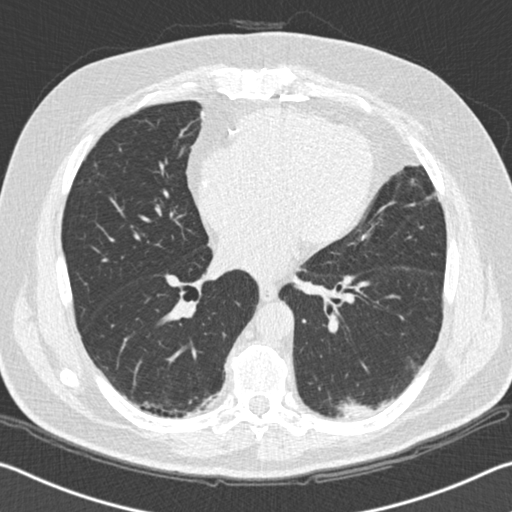
Chest CT (low-dose screening protocol), one axial image, second screening round (one year after baseline), lung window (W 1500 / L -600 HU), standard (soft-tissue) reconstruction kernel (B30f), 120 kVp, slice 91 of 172 in the series, 512 × 512 image matrix. Male, age 65 years at enrolment. Former smoker at enrolment.
Lesion marked by an expert reader, bounding box [x1, y1, x2, y2] px = [325, 389, 392, 434]. Reader record for this screening exam (exam-level; its link to the box is not recorded): non-calcified nodule or mass ≥4 mm, left lower lobe, 19 × 11 mm, spiculated (stellate) margins, soft tissue attenuation, pre-existing on the prior screen: yes; interval growth: yes. Official screen result: positive, change unspecified: nodule(s) >= 4 mm or enlarging nodule(s), mass(es), or other non-specific abnormalities suspicious for lung cancer.